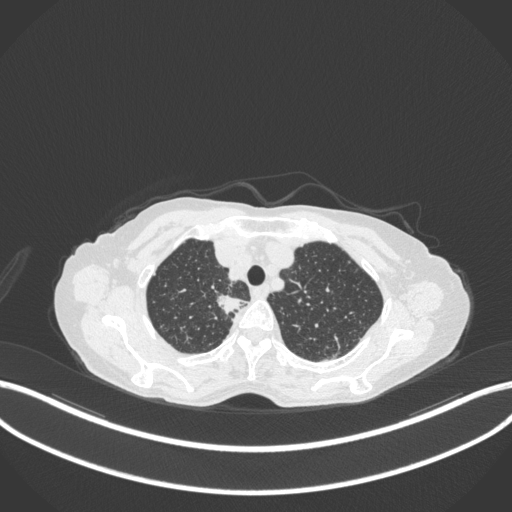
Chest CT, one axial slice; slice 311 of 363 in the series (ordered by position); reconstruction kernel B31f; 120 kVp; lung window (W 1500 / L -600 HU); 1 mm slice thickness; 512 × 512 image matrix, field of view 400 × 400 mm. Female patient, age 75 years. Case-level facts recorded for this patient, not image findings: clinical TNM (as recorded): T1c N1 M1.
Annotated regions visible in this slice (bounding box drawn by a radiologist):
- lung tumour (recorded histology: adenocarcinoma): box from (x=215, y=291) to (x=246, y=314) px